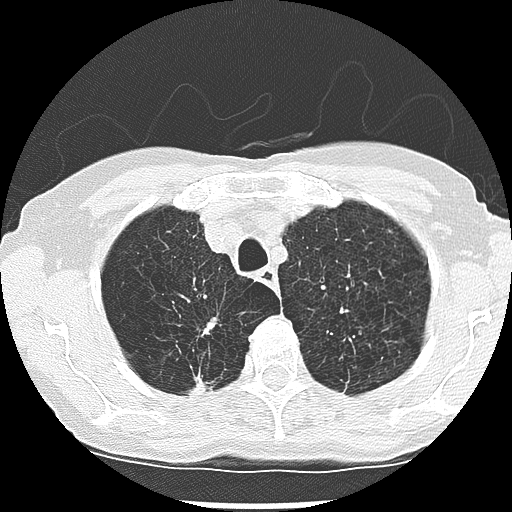
Low-dose screening chest CT, one axial slice; slice 224 of 265 in the series (ordered by position); reconstruction kernel LUNG; 120 kVp; lung window (W 1500 / L -600 HU); 512 × 512 image matrix, field of view 300 × 300 mm.
Outlined on this slice (expert manual segmentation):
- lesion 1 (nodule, upper lobe of right lung): bounding box [x1, y1, x2, y2] px = [191, 375, 207, 394]
- lesion 2 (tumor, upper lobe of right lung): [205, 324, 214, 333]